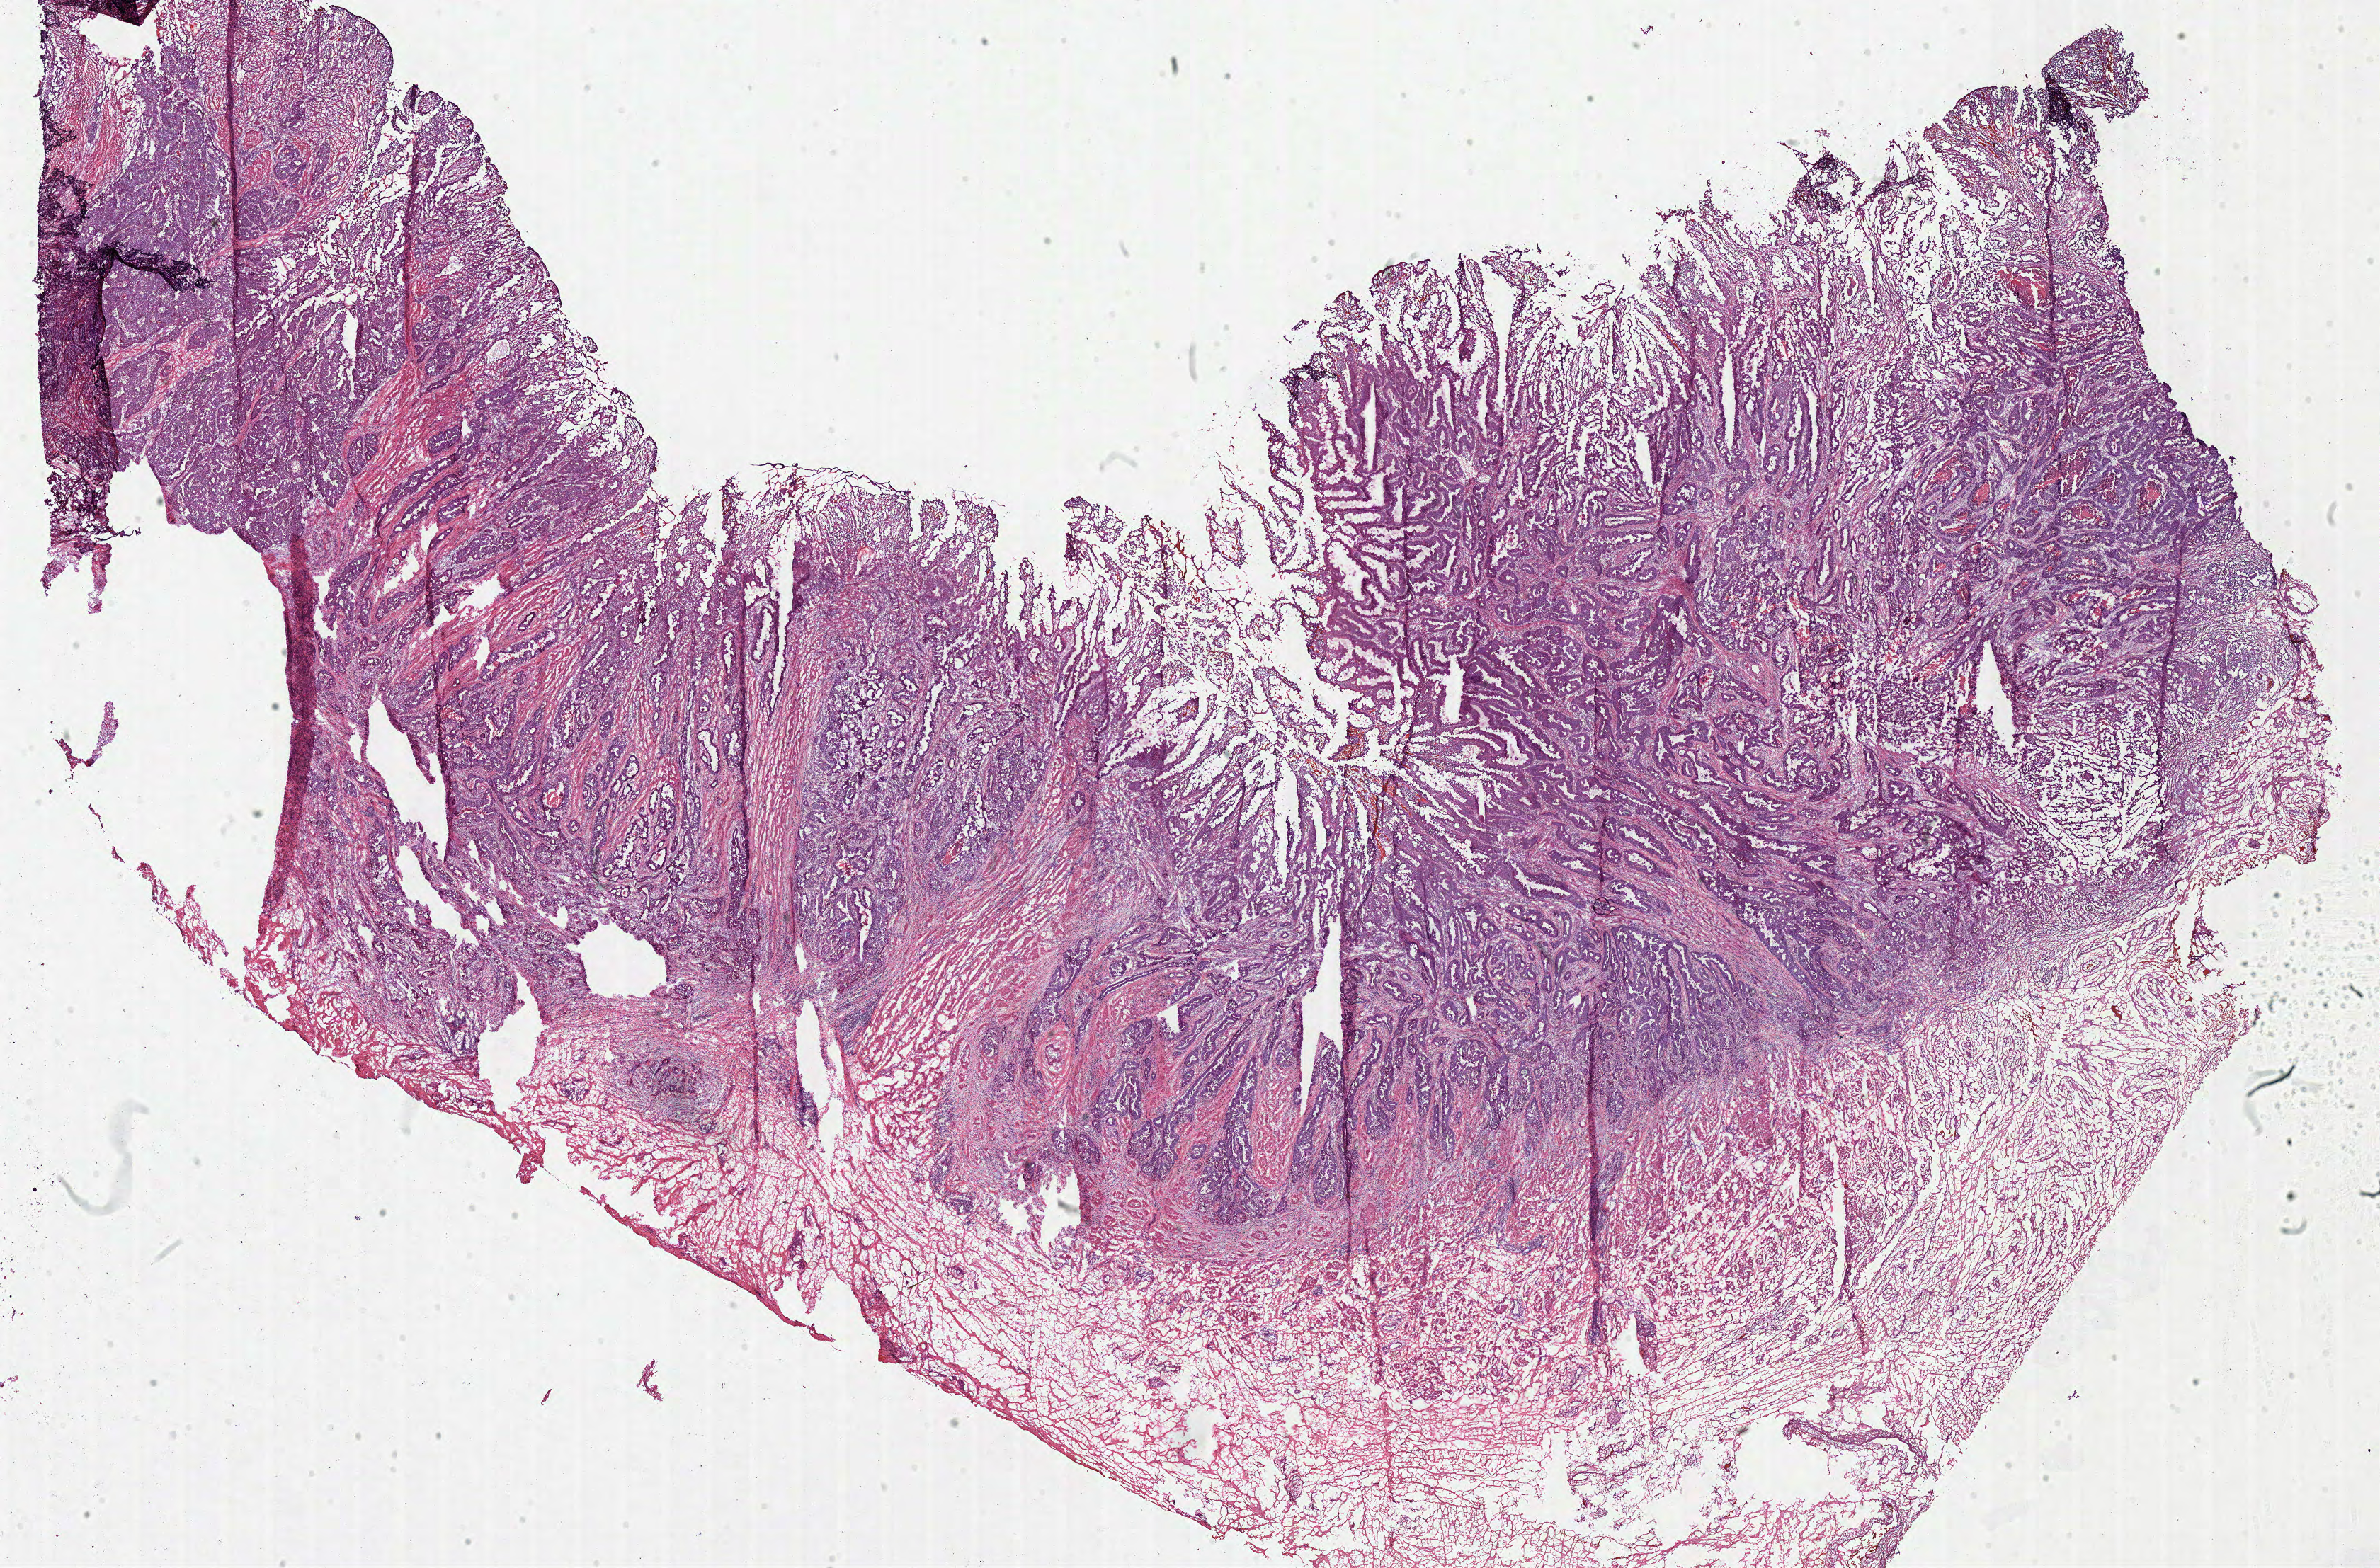
Whole-slide histology image, H&E, a low-resolution overview of the entire scanned area, about 26.4 x 17.4 mm (from a 40x scan), frozen section, rectum, primary tumour sample. Female, age 62 years at initial diagnosis. Slide review estimates, as recorded: tumour cells 70%, tumour nuclei 80%, normal cells 0%, stromal cells 20%, necrosis 10%.
• AJCC pathologic stage: IIA
• lymph nodes positive (case pathology): 0 of 2 examined
• diagnosis: Adenocarcinoma, NOS